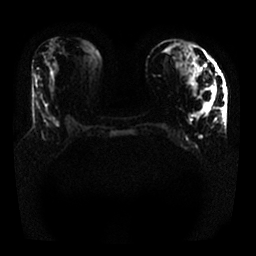
Breast MRI, one axial slice; position 7 of 25 along the scan axis; diffusion-weighted series; image 2 of 4 stored at this slice position (different b-values; order by instance number); 1.5 T; 4 mm slice thickness; 256 × 256 image matrix. Female patient.
Outlined on this slice (manually delineated by an expert):
- tumour on diffusion-weighted imaging: bounding box [x1, y1, x2, y2] px = [200, 88, 216, 116]